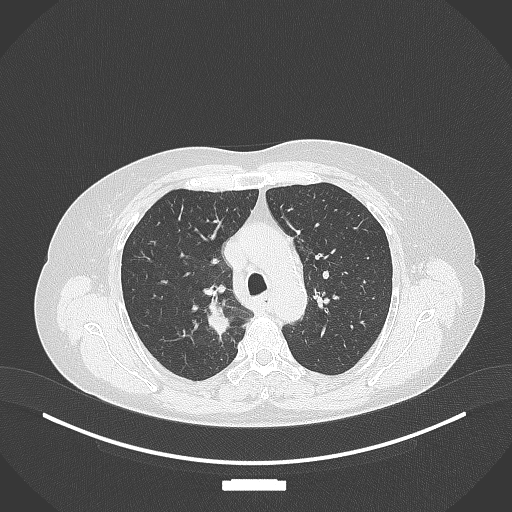
Chest CT, one axial slice; reconstruction kernel B70f; lung window (W 1500 / L -600 HU); 1 mm slice thickness; 512 × 512 image matrix, field of view 400 × 400 mm. Female patient, age 62 years. From the clinical record (not read from this slice): clinical TNM (as recorded): T1c N1 M0.
Structures marked on this image (rectangle marked by the reading radiologist):
- lung tumour (recorded histology: squamous cell carcinoma): bounding box [x1, y1, x2, y2] px = [205, 295, 231, 336]